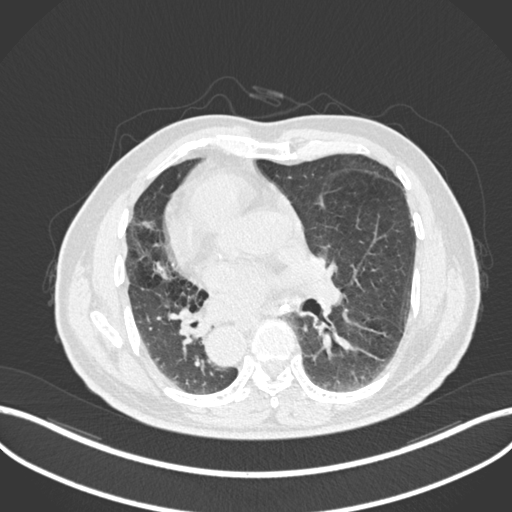
Chest CT, one axial slice. Slice 106 of 206 in the series (ordered by position). Lung window (W 1500 / L -600 HU). 1 mm slice thickness. 512 × 512 image matrix. Male patient, age 67 years. Case-level facts recorded for this patient, not image findings: clinical TNM (as recorded): T2a N0 M0.
Outlined on this slice (bounding box drawn by a radiologist):
- lung tumour (recorded histology: squamous cell carcinoma): bounding box <165,304,213,343> (left, top, right, bottom; pixels)